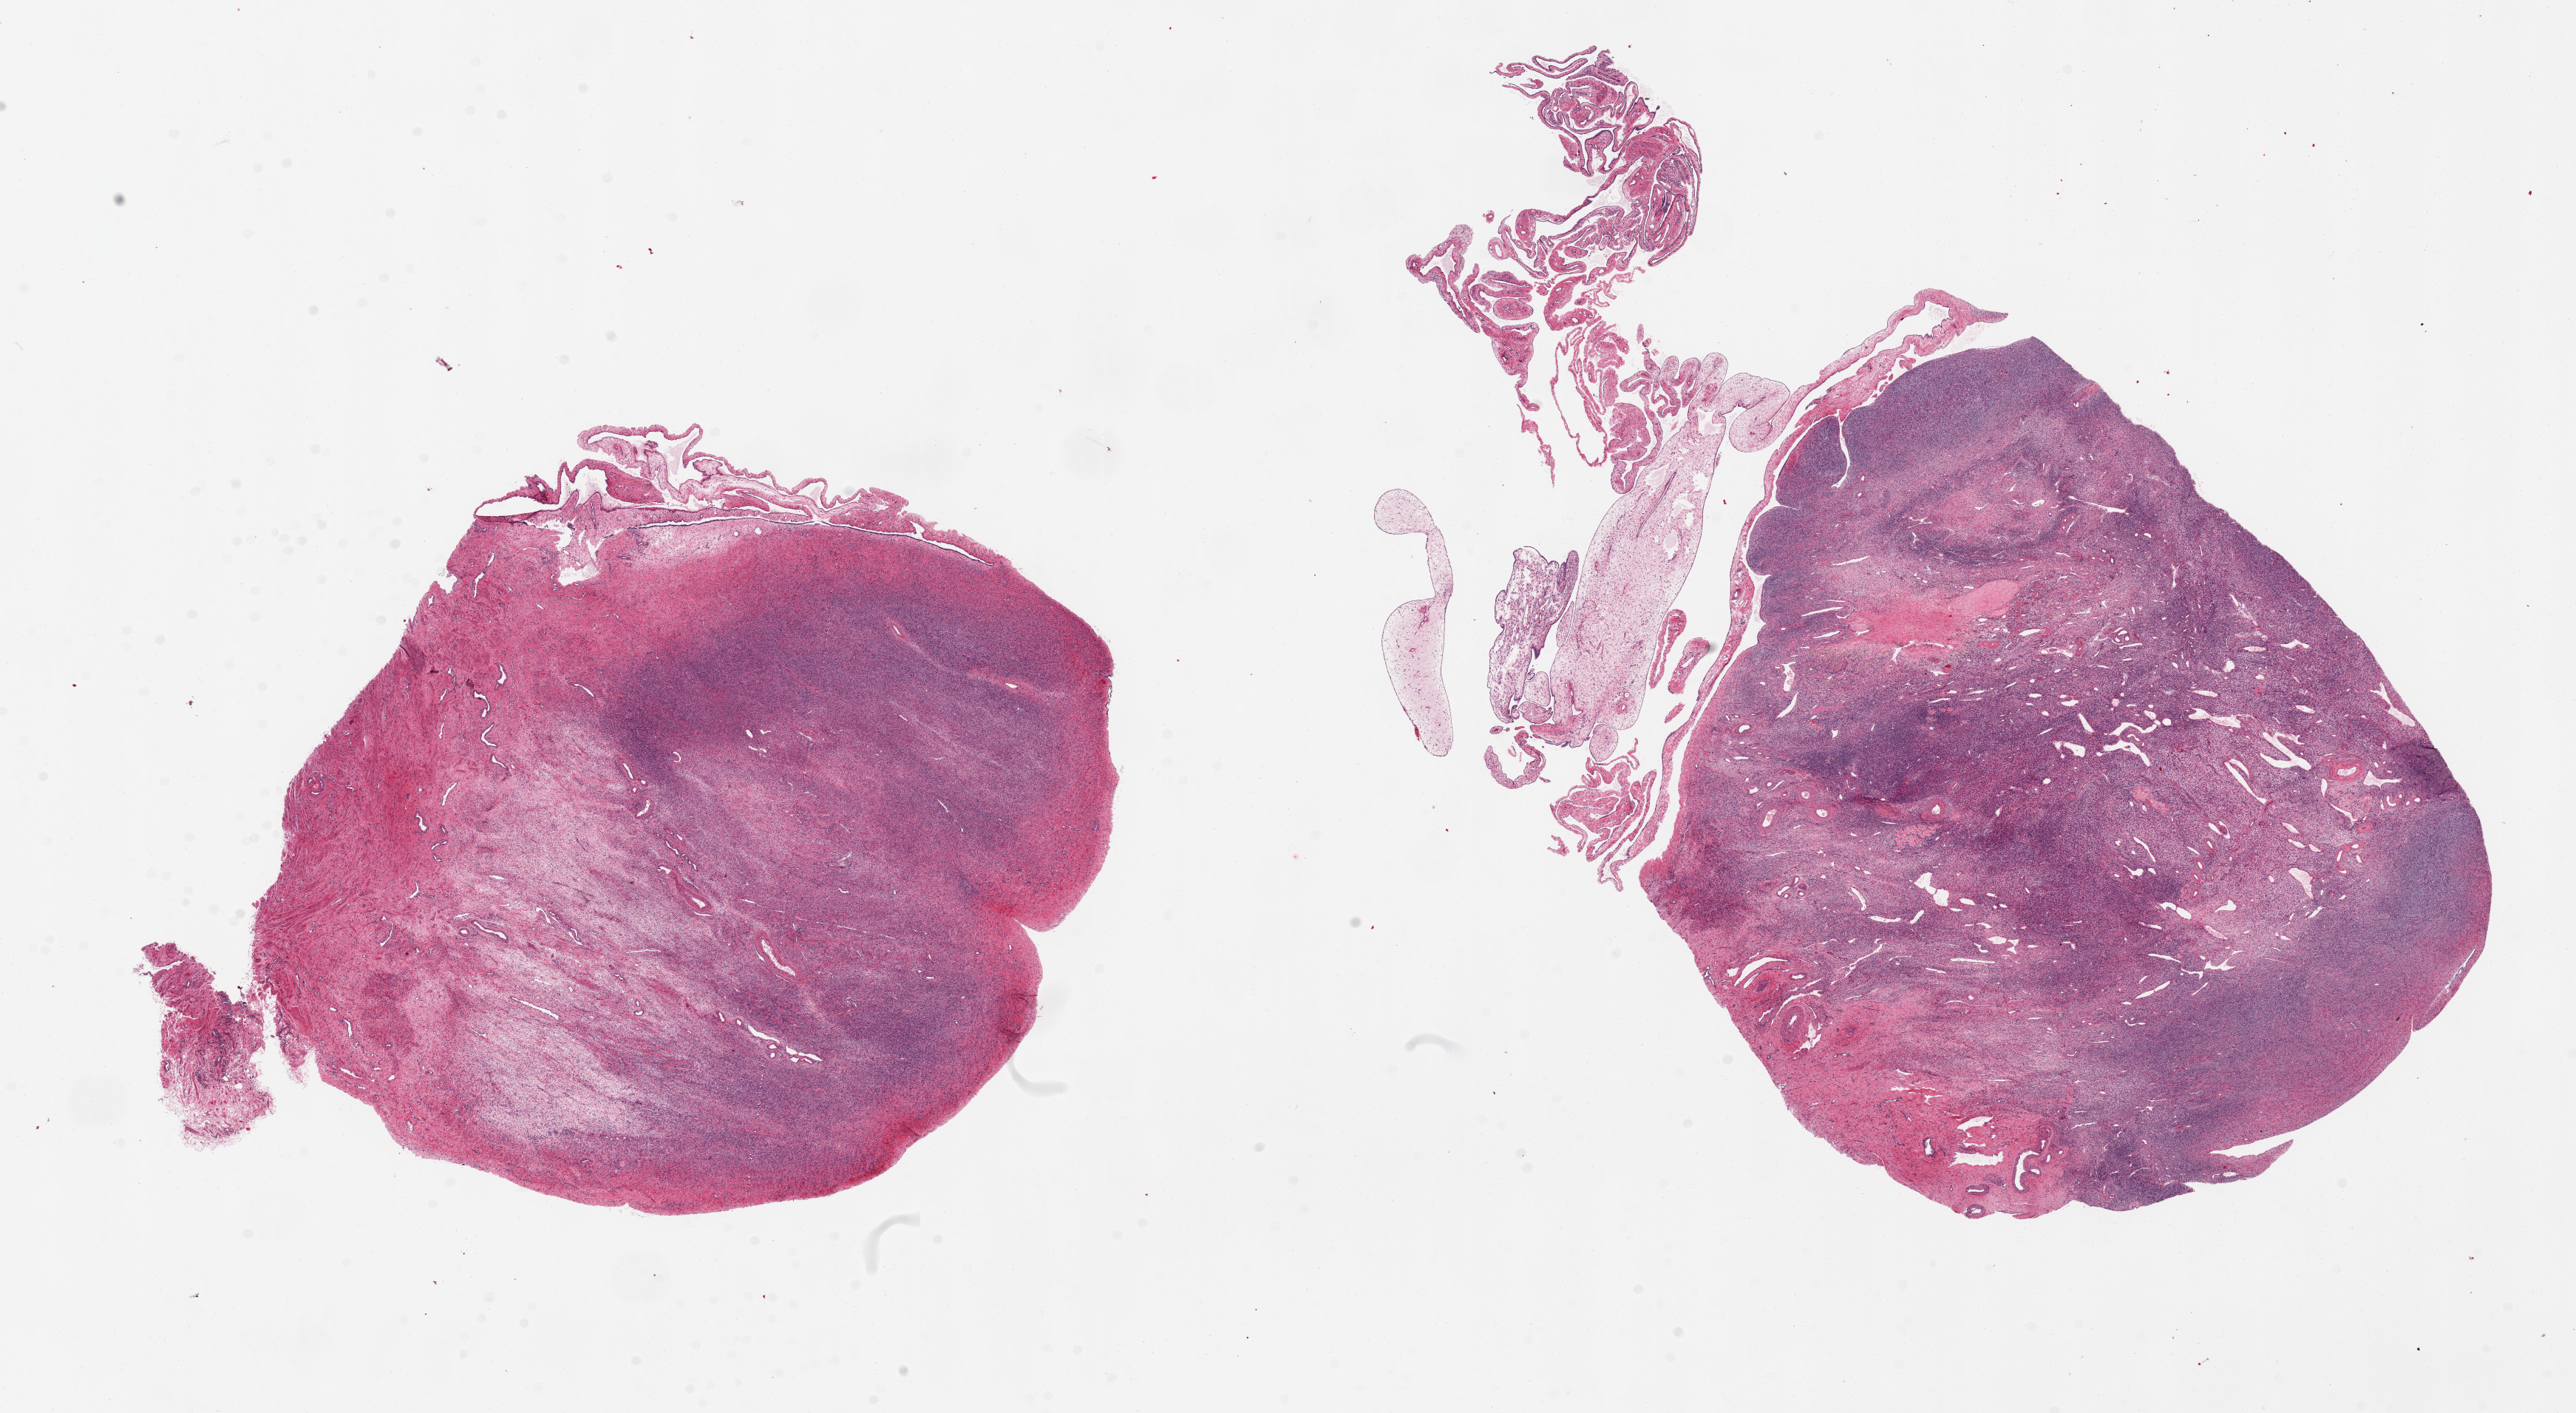
Whole-slide image, hematoxylin and eosin (H&E) stain, whole scanned area (about 27.6 x 15.1 mm, slide scanned at 20x) shown as a low-resolution overview, PAXgene-fixed, paraffin-embedded tissue, sampled site (target tissue): ovary, donor tissue sample. Female donor.
Pathologist's review note for this sample: 2 pieces. 9x9 & 14x8mm; Inactive. 1 has adherent stroma.